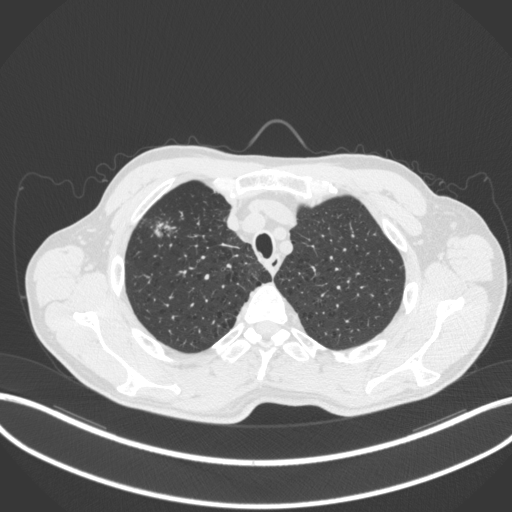
Chest CT, one axial slice; slice 352 of 414 in the series (ordered by position); reconstruction kernel B31f; 120 kVp; lung window (W 1500 / L -600 HU); 1 mm slice thickness; 512 × 512 image matrix, field of view 400 × 400 mm. Patient: male, 69 years. Case-level facts recorded for this patient, not image findings: clinical TNM (as recorded): T1b N1 M0.
Outlined on this slice (bounding box drawn by a radiologist):
- lung tumour (recorded histology: adenocarcinoma): bounding box <155,216,182,240> (left, top, right, bottom; pixels)